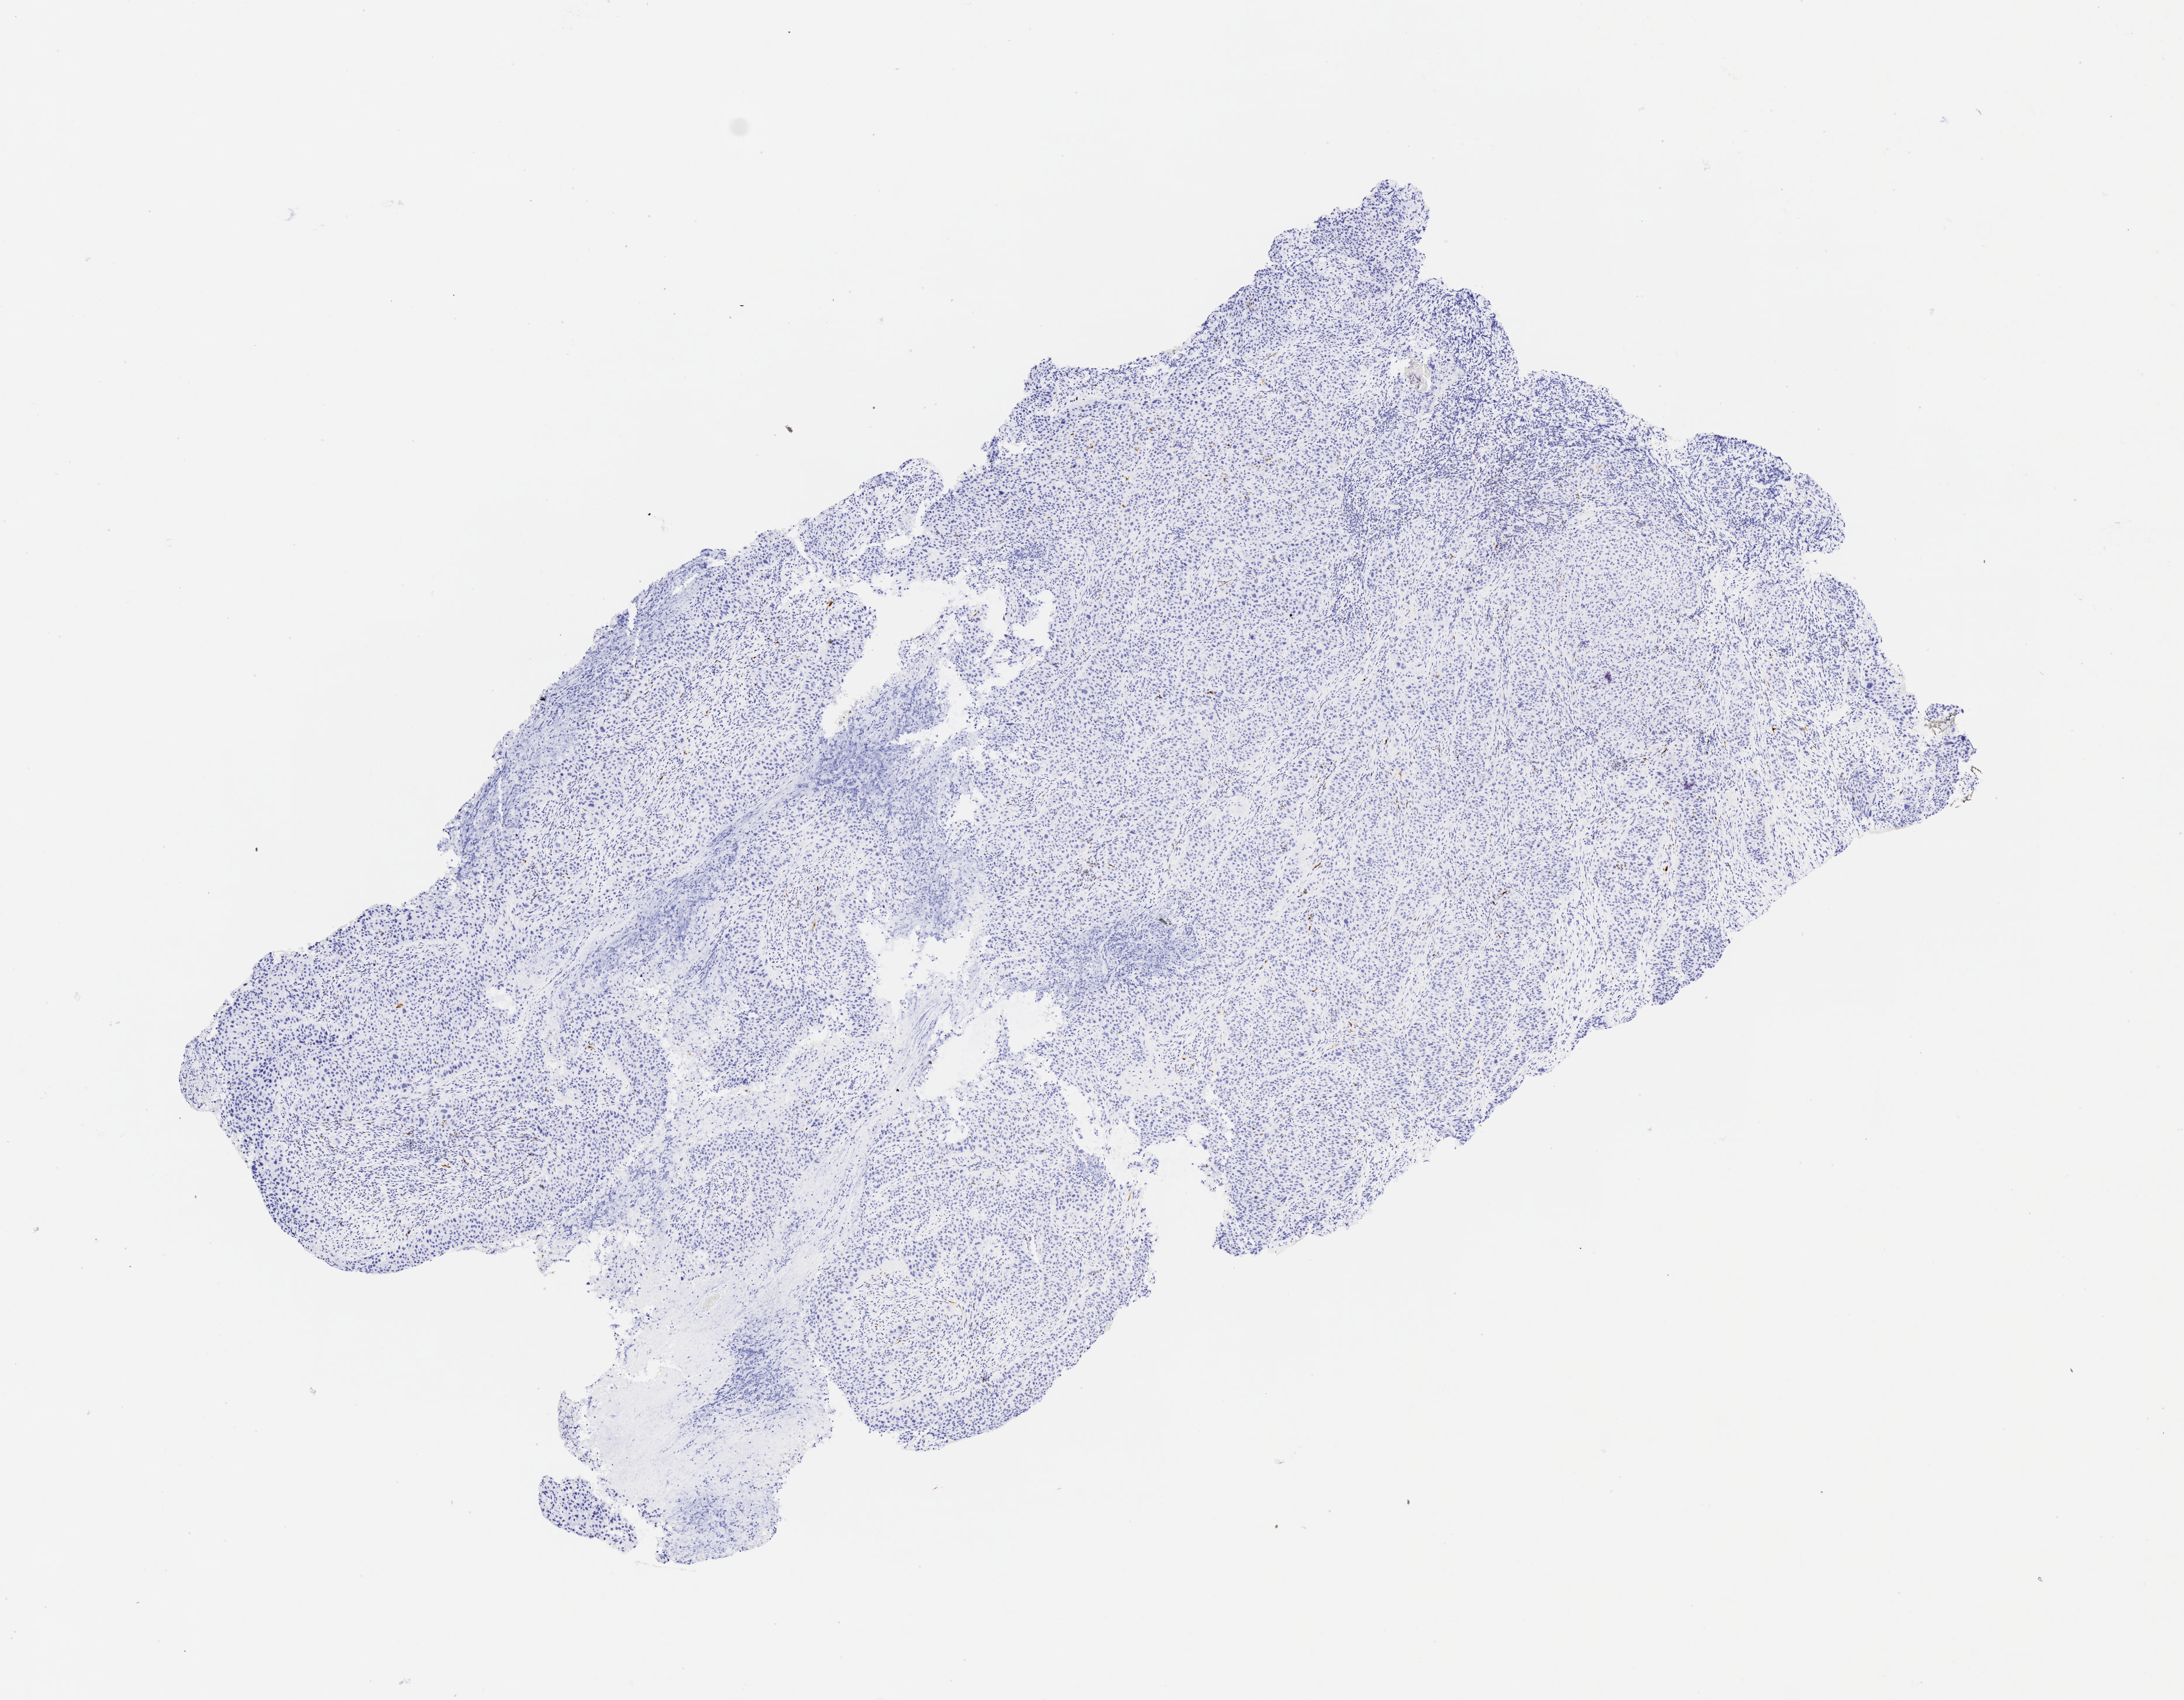
Whole-slide image, immunohistochemical stain for p16 (p16INK4a), whole scanned area (about 7.5 x 5.9 mm) shown as a low-resolution overview; specimen: tumor tissue; anatomic site: cervix. Female patient, aged 48.
* histologic diagnosis: Squamous cell carcinoma, large cell, nonkeratinizing, NOS